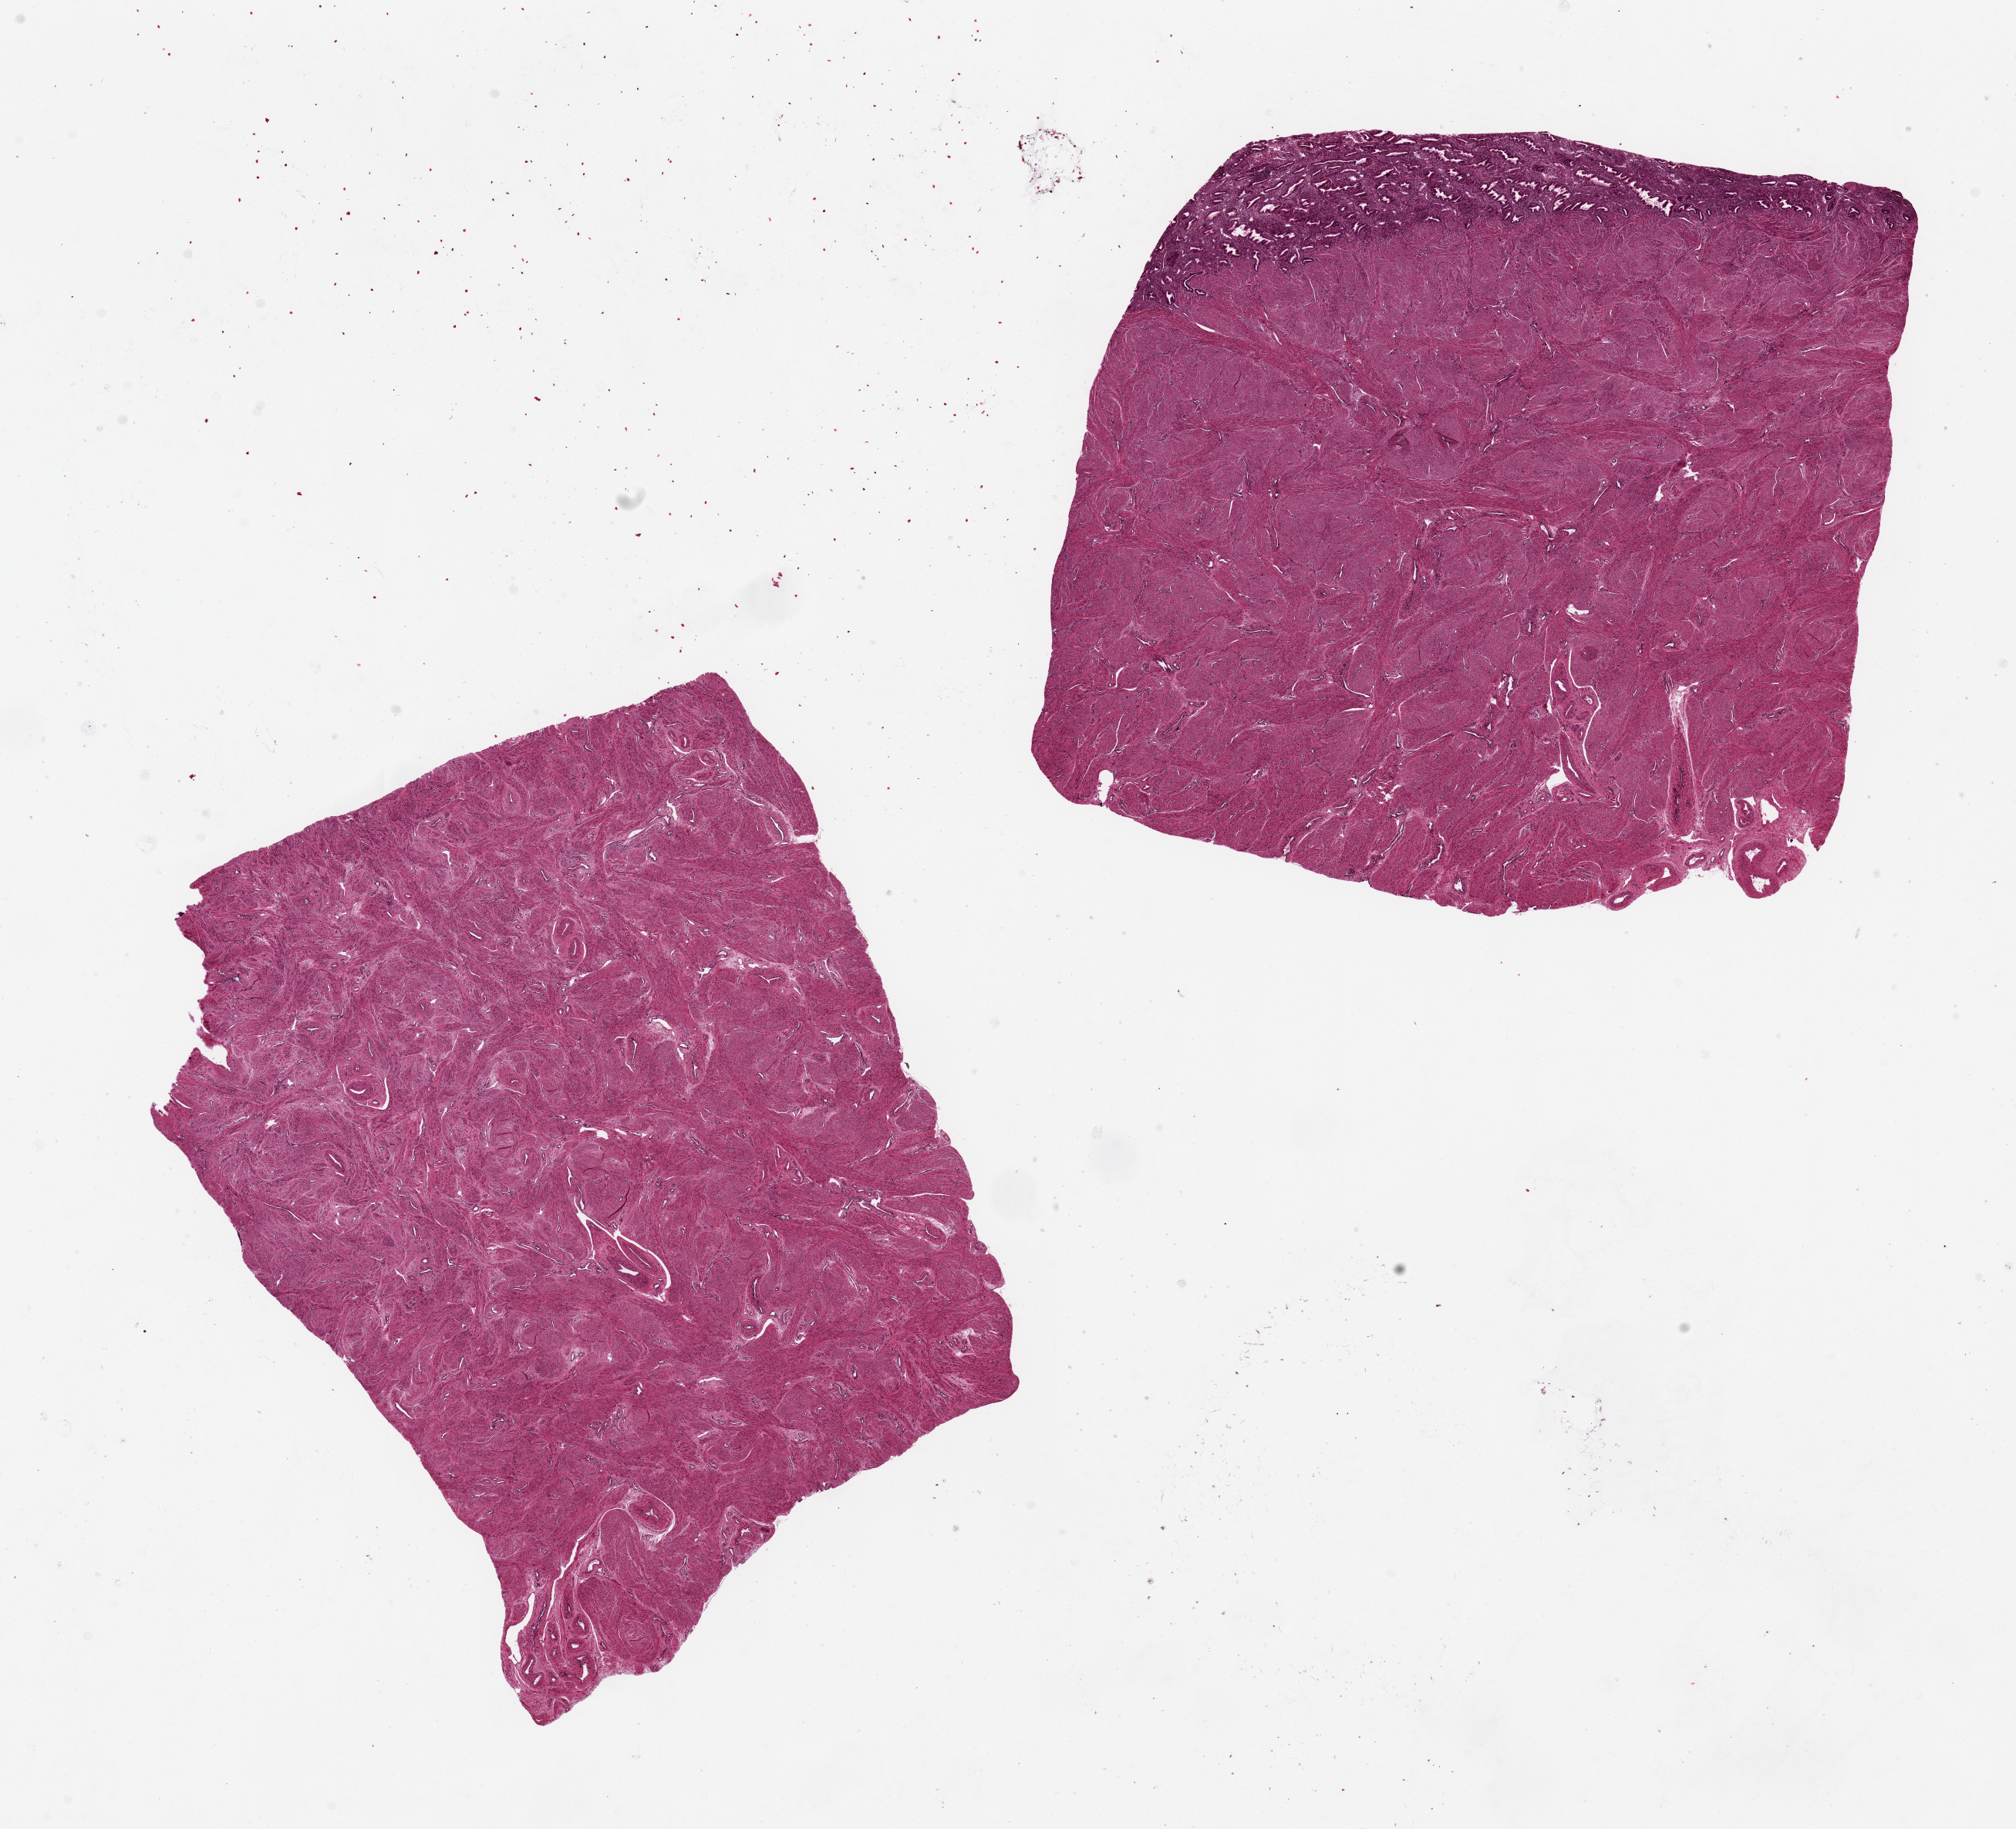
Whole-slide image, haematoxylin and eosin stain, brightfield, shown as a low-resolution overview of the whole scanned area (about 20.7 x 18.8 mm); PAXgene-fixed paraffin-embedded (PFPE) section; sampled site (target tissue): uterus; donor tissue sample.
Pathologist's review note for this sample: 2 pieces, ~ 8x7mm, one with layer of proliferative endometrium along one edge, well- preserved.